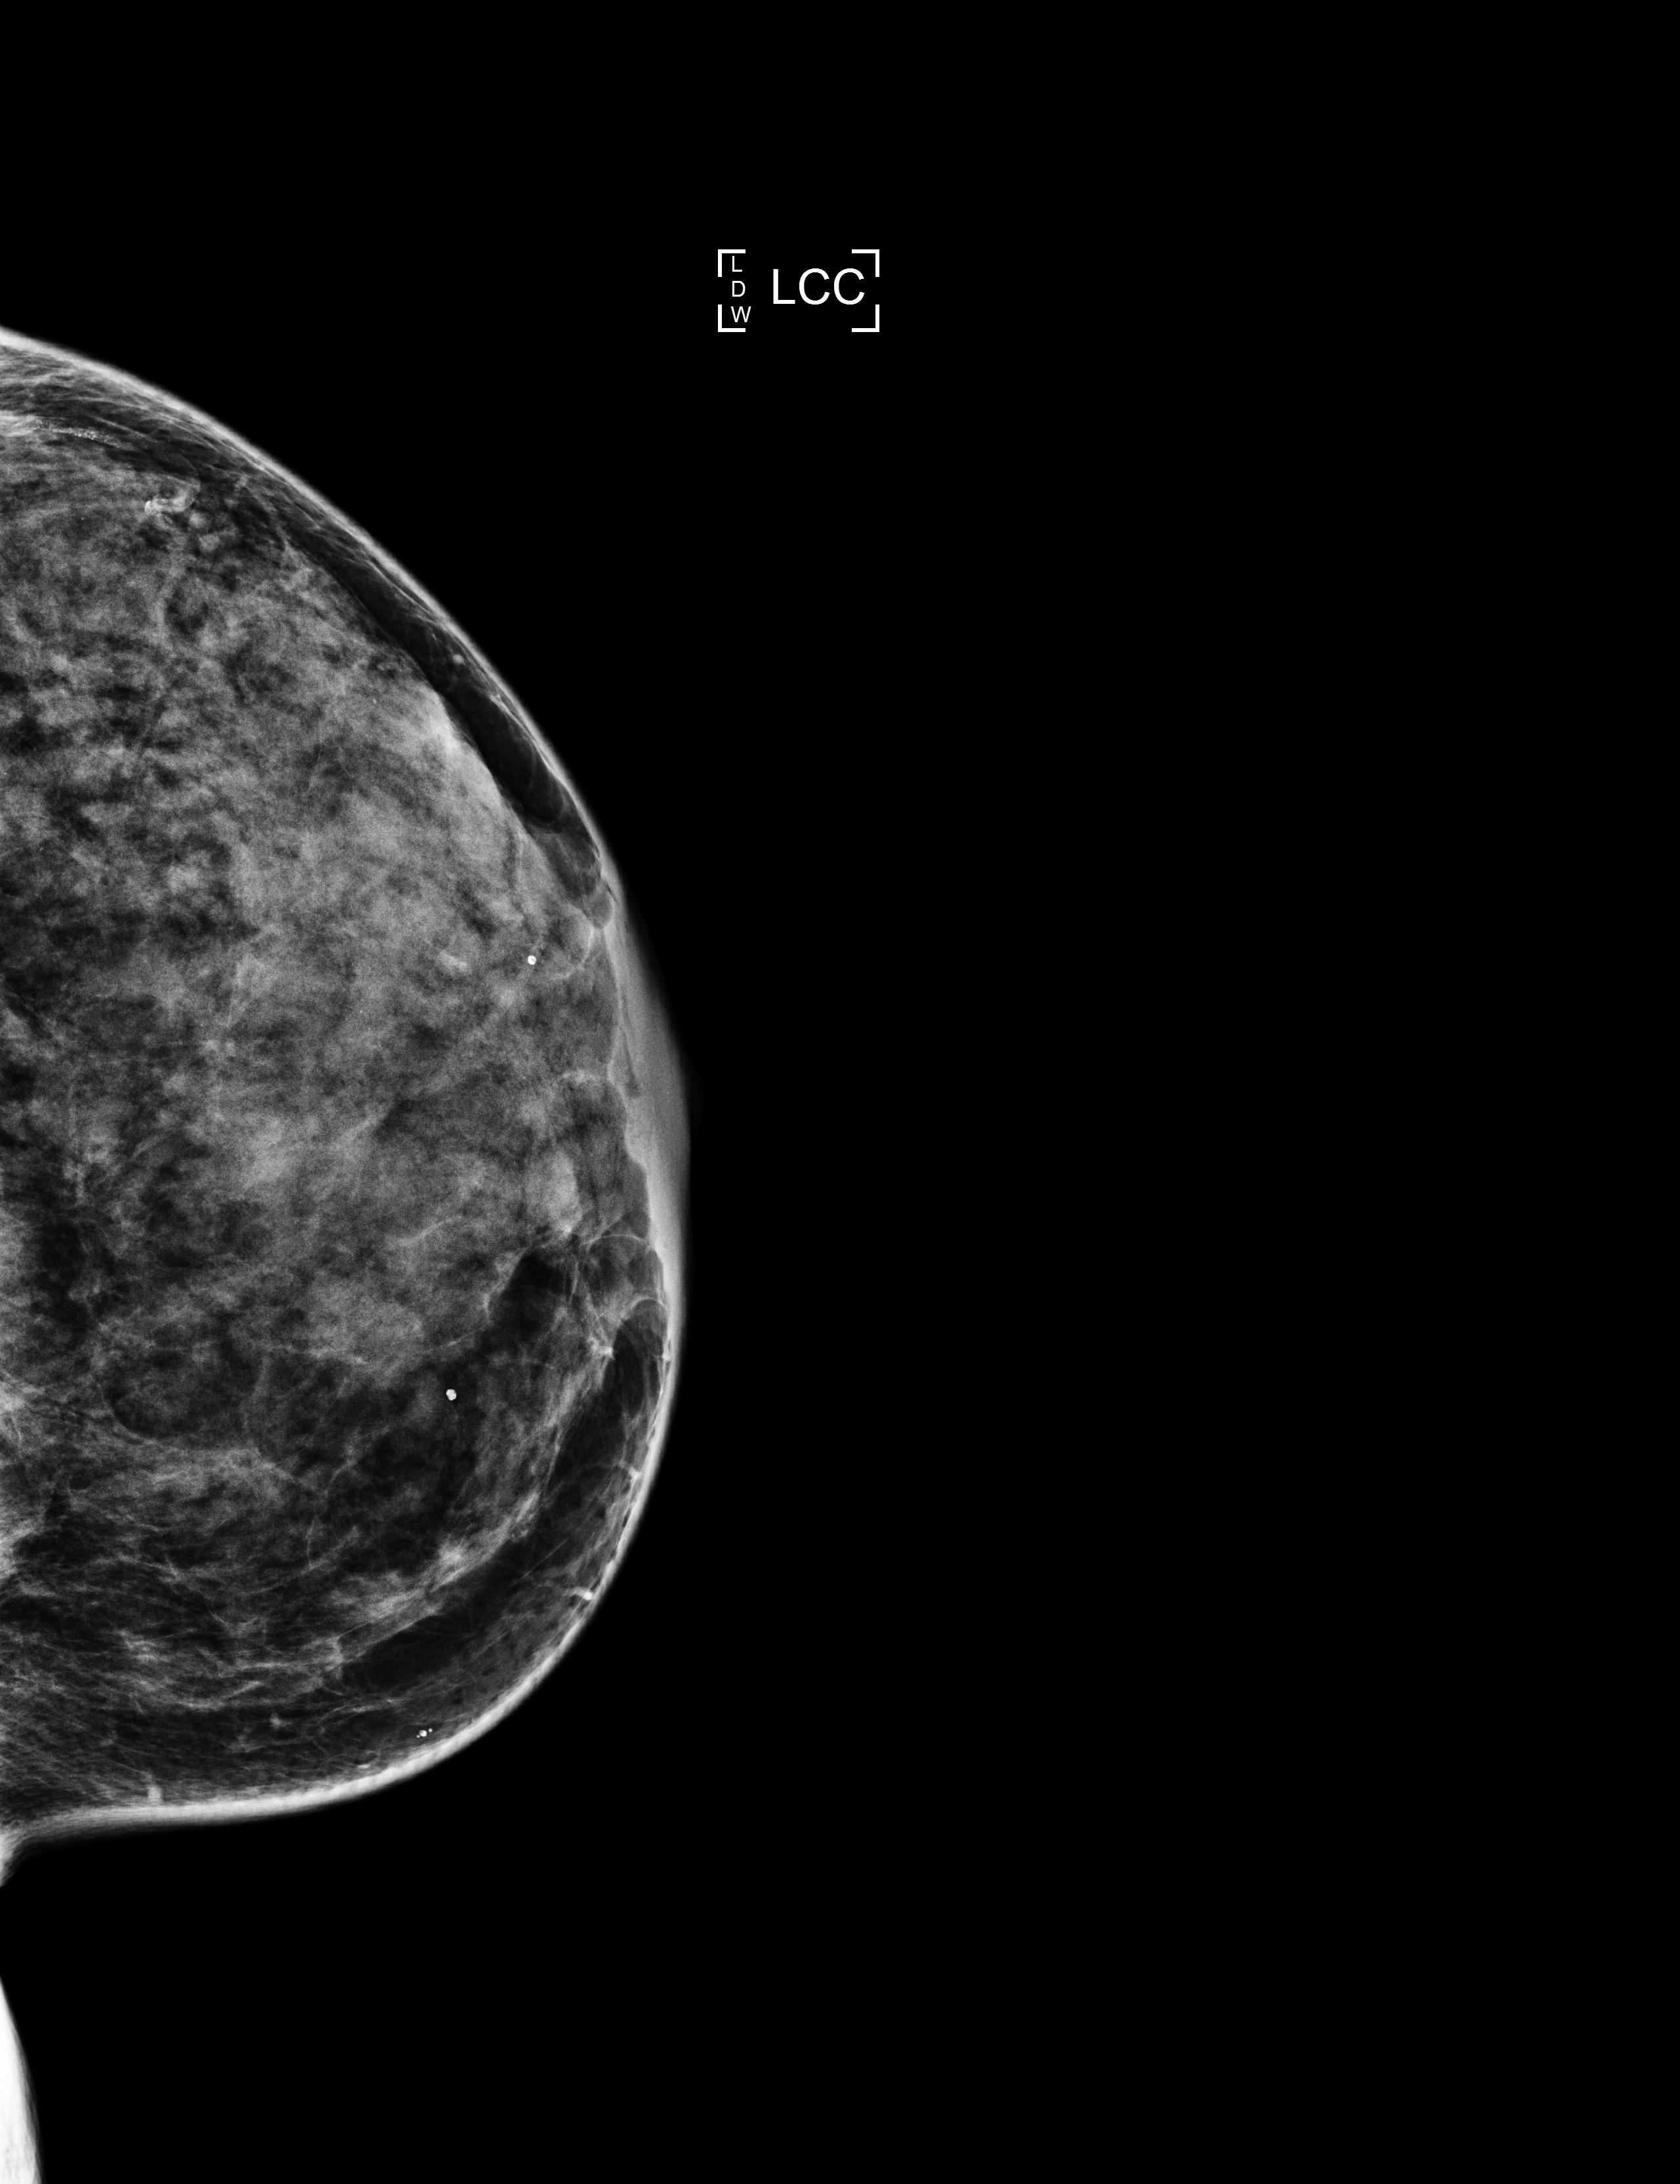
Annual screening mammography examination. Patient aged 57 years (female).
Image type: full-field digital mammogram. Breast: left. Projection: CC view.